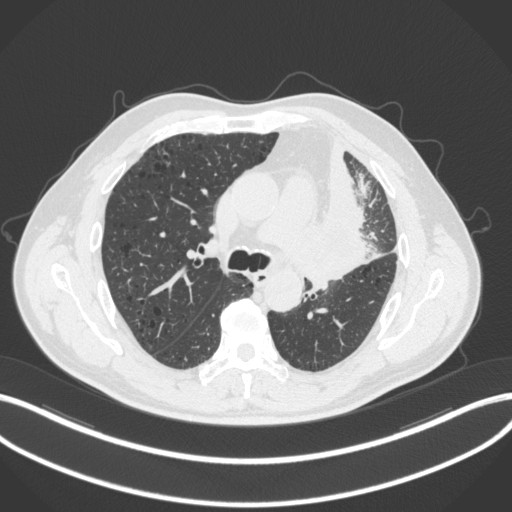
Chest CT, one axial slice; position 181 of 286 along the scan axis; lung window (W 1500 / L -600 HU); 512 × 512 image matrix, field of view 400 × 400 mm. Patient: male, 68 years. Case-level facts recorded for this patient, not image findings: clinical TNM (as recorded): T3 N3 M1.
Annotated regions visible in this slice (rectangle marked by the reading radiologist):
- lung tumour (recorded histology: adenocarcinoma): bounding box <319,189,373,283> (left, top, right, bottom; pixels)